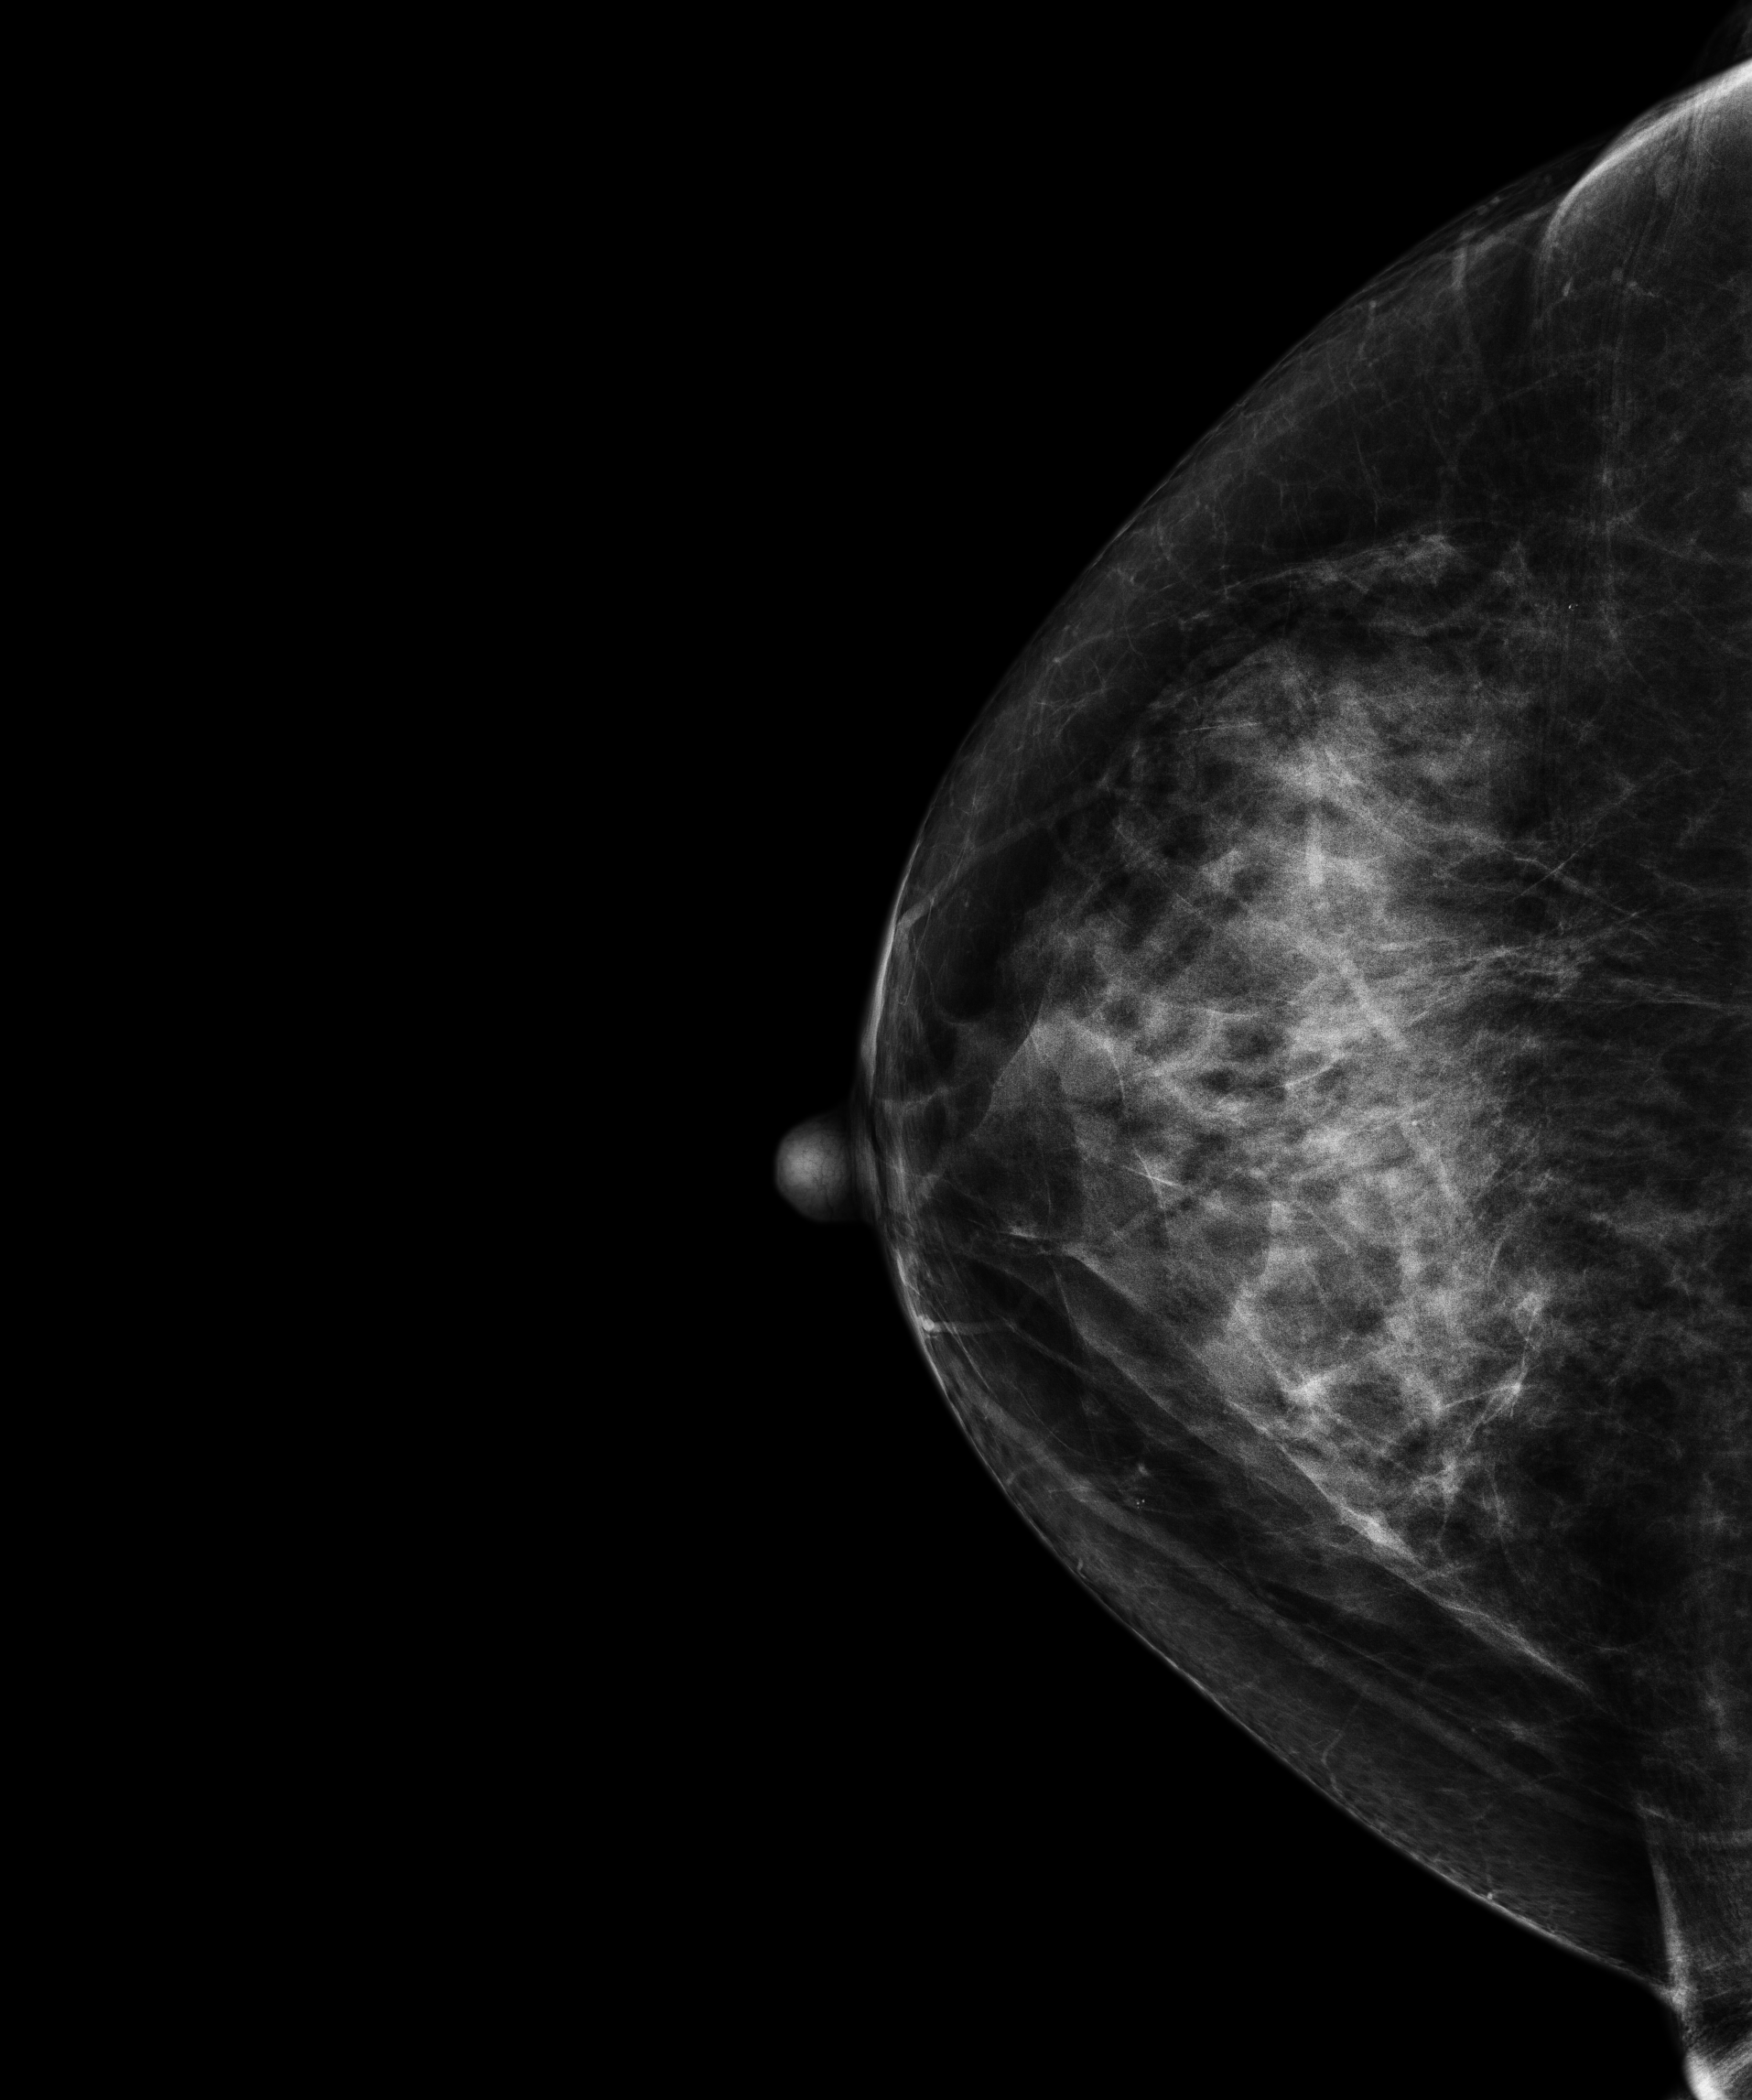
Annual screening mammography examination. Patient: female, 68 years.
Image type: full-field digital mammogram. Breast: right. Projection: craniocaudal (CC) view.